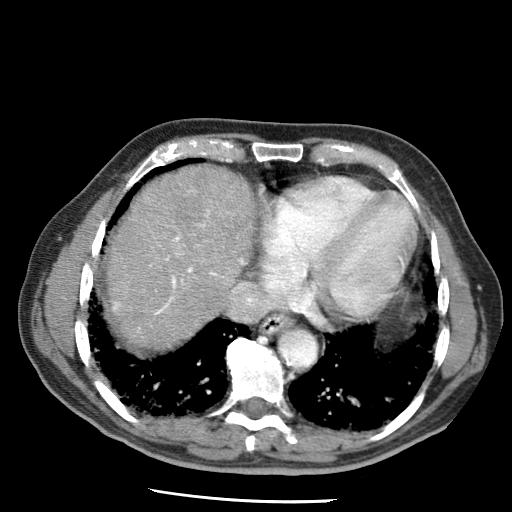
Contrast-enhanced abdominal CT (liver protocol), one axial slice. Position 60 of 79 along the scan axis. Soft-tissue window (W 400 / L 40 HU). 512 × 512 image matrix, field of view 320 × 320 mm. Case-level facts recorded for this patient, not image findings: diagnosis: hepatocellular carcinoma (patient treated with transarterial chemoembolisation; whether this scan precedes or follows treatment is not stated here); TNM stage (as recorded): Stage-IIIA; Child-Pugh class: A; tumour differentiation: moderately differentiated.
Outlined on this slice (semi-automatic segmentation, software-assisted and operator-edited):
- liver parenchyma outside the tumour (the mass and vessels are separate outlines, so this box may not span the whole liver): bounding box <108,168,254,348> (left, top, right, bottom; pixels)
- liver vessels: <113,191,244,315>